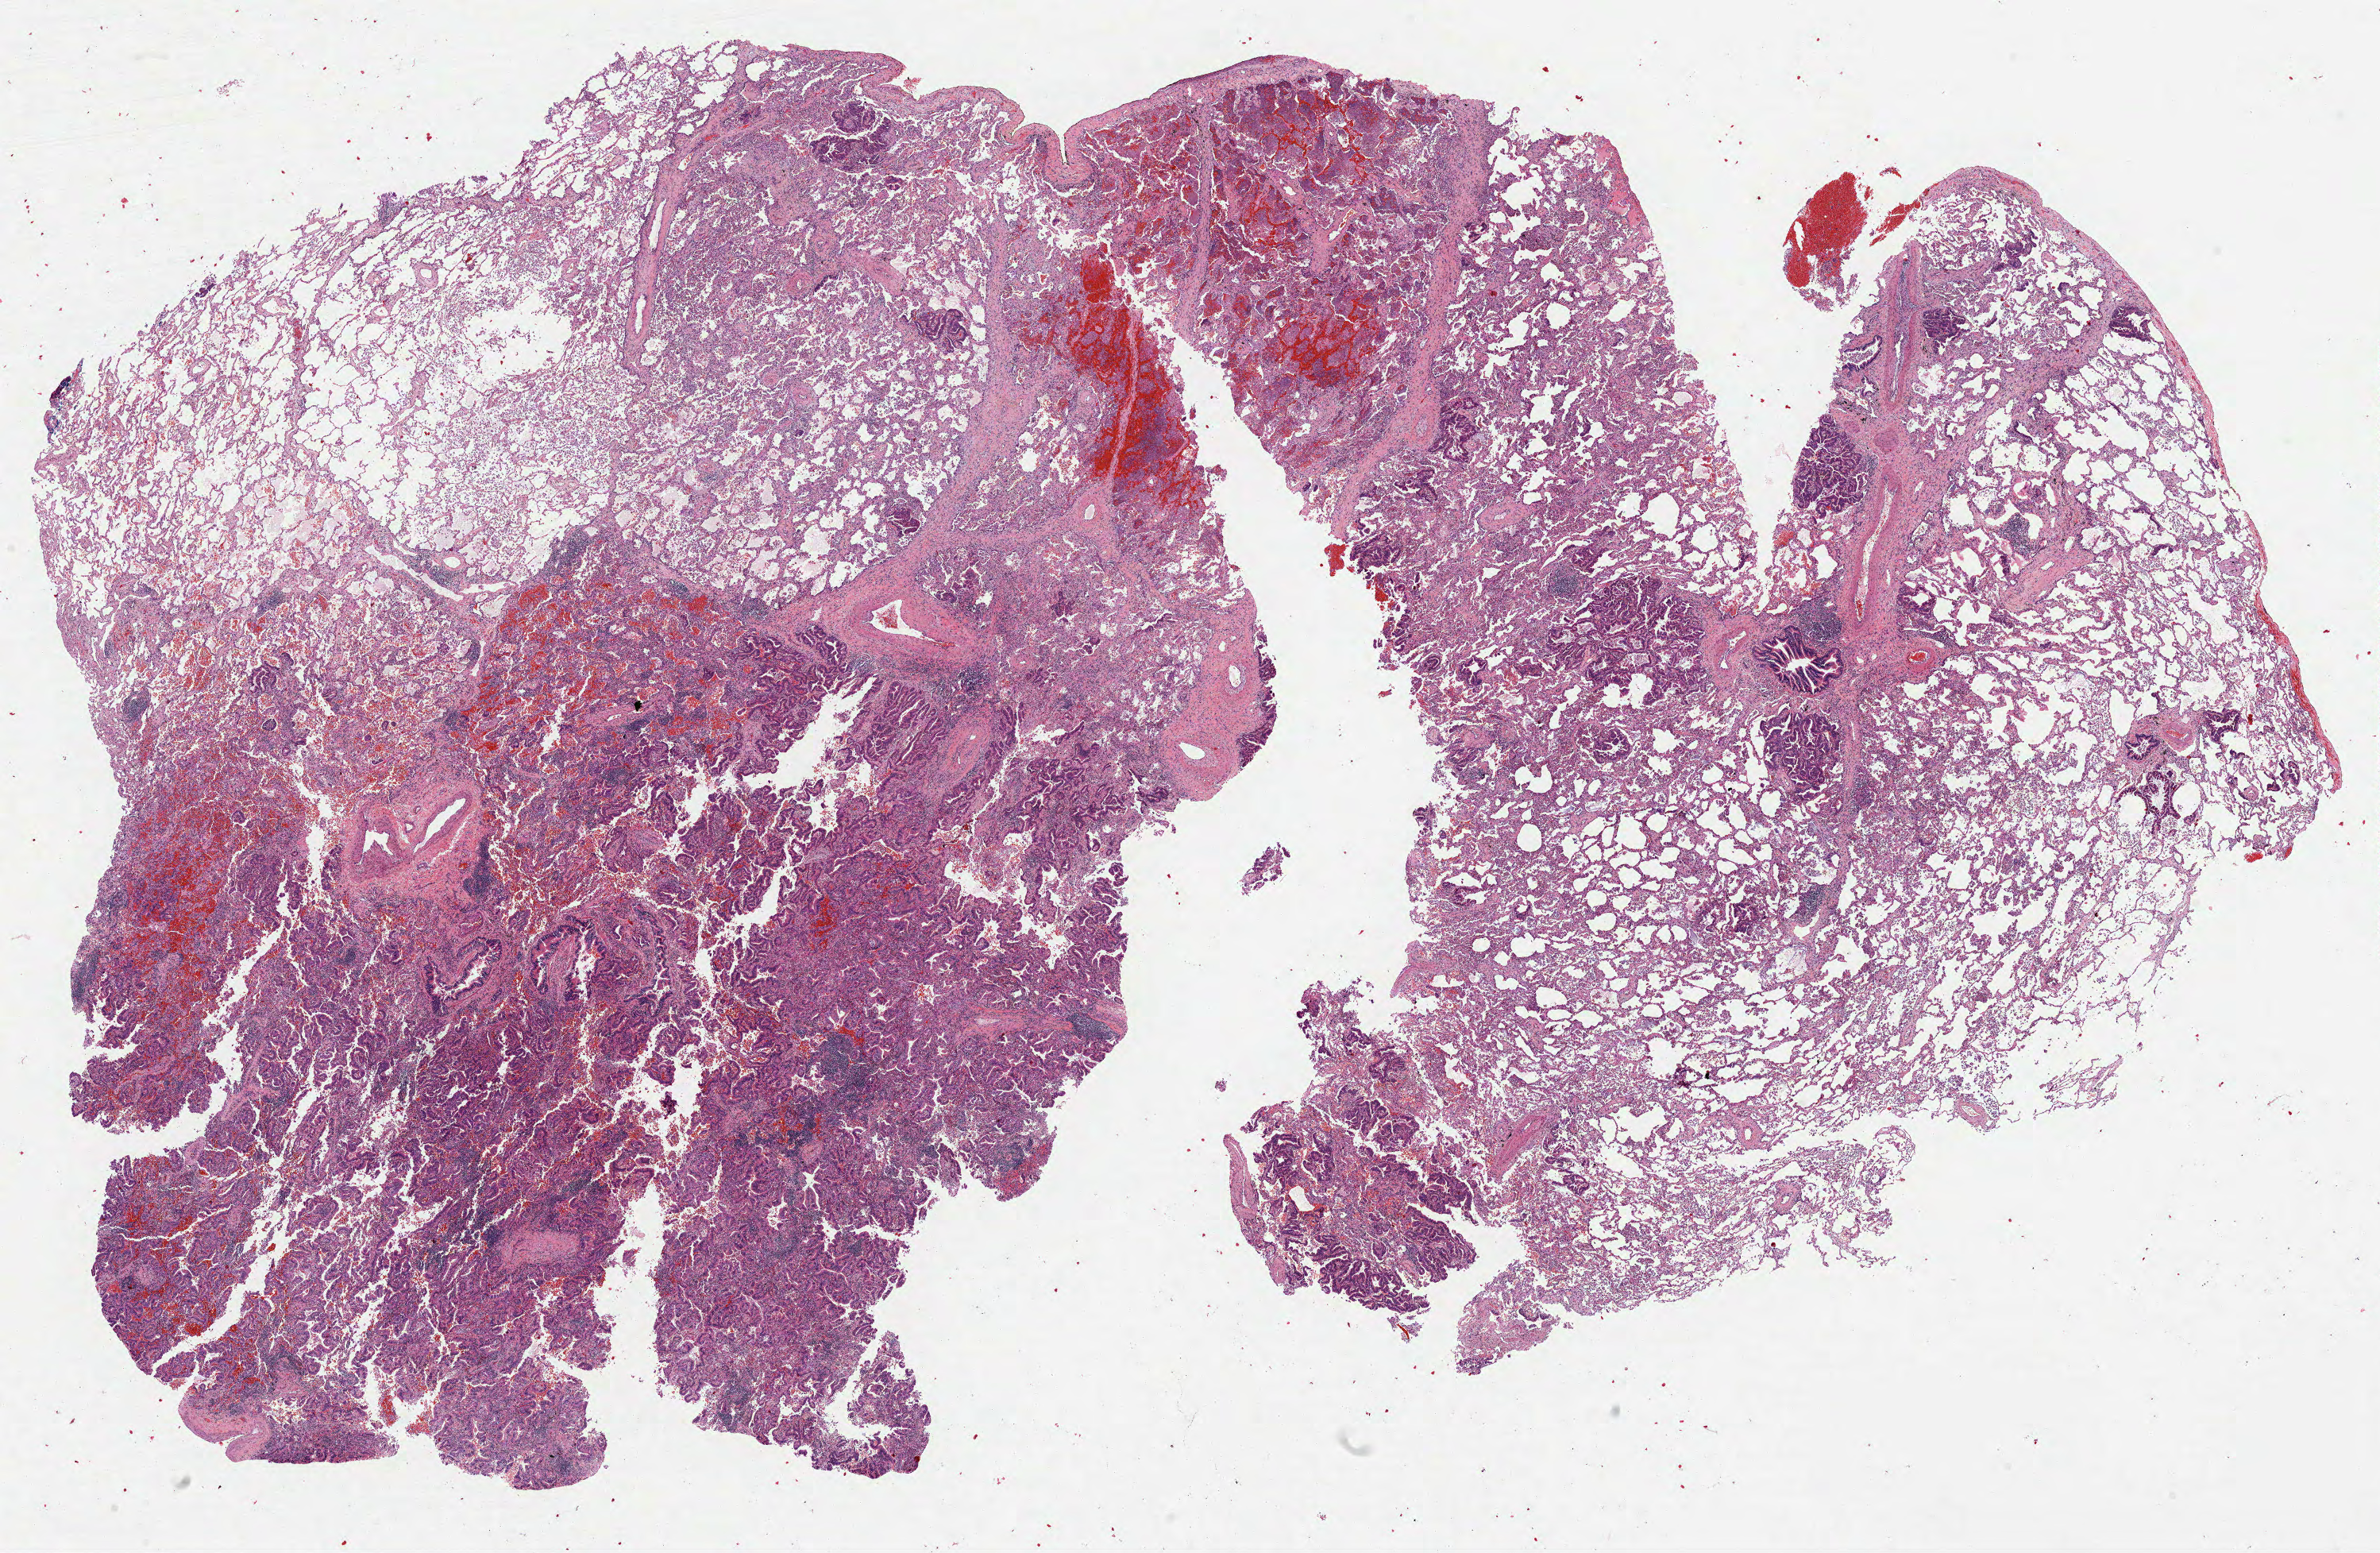
H&E-stained whole-slide image, low-resolution overview of the scanned area, about 24.2 x 15.8 mm; formalin-fixed paraffin-embedded (FFPE) diagnostic section; lung, primary tumour sample. Female patient; age at initial diagnosis 71 years.
- AJCC pathologic stage: IIB
- histologic diagnosis: Adenocarcinoma, NOS